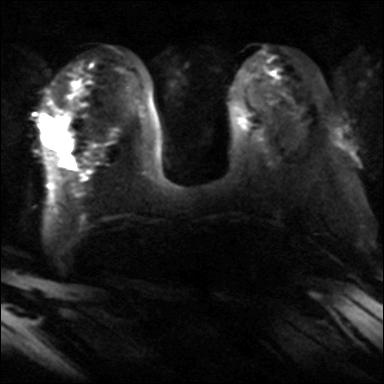
Breast MRI, one axial slice. Slice 14 of 40 in the series (ordered by position). Diffusion-weighted series; image 2 of 4 stored at this slice position (different b-values; order by instance number). 3 T. 384 × 384 image matrix. Female patient.
Structures marked on this image (outlined manually by an expert reader):
- tumour on diffusion-weighted imaging: bounding box [x1, y1, x2, y2] px = [52, 123, 75, 148]